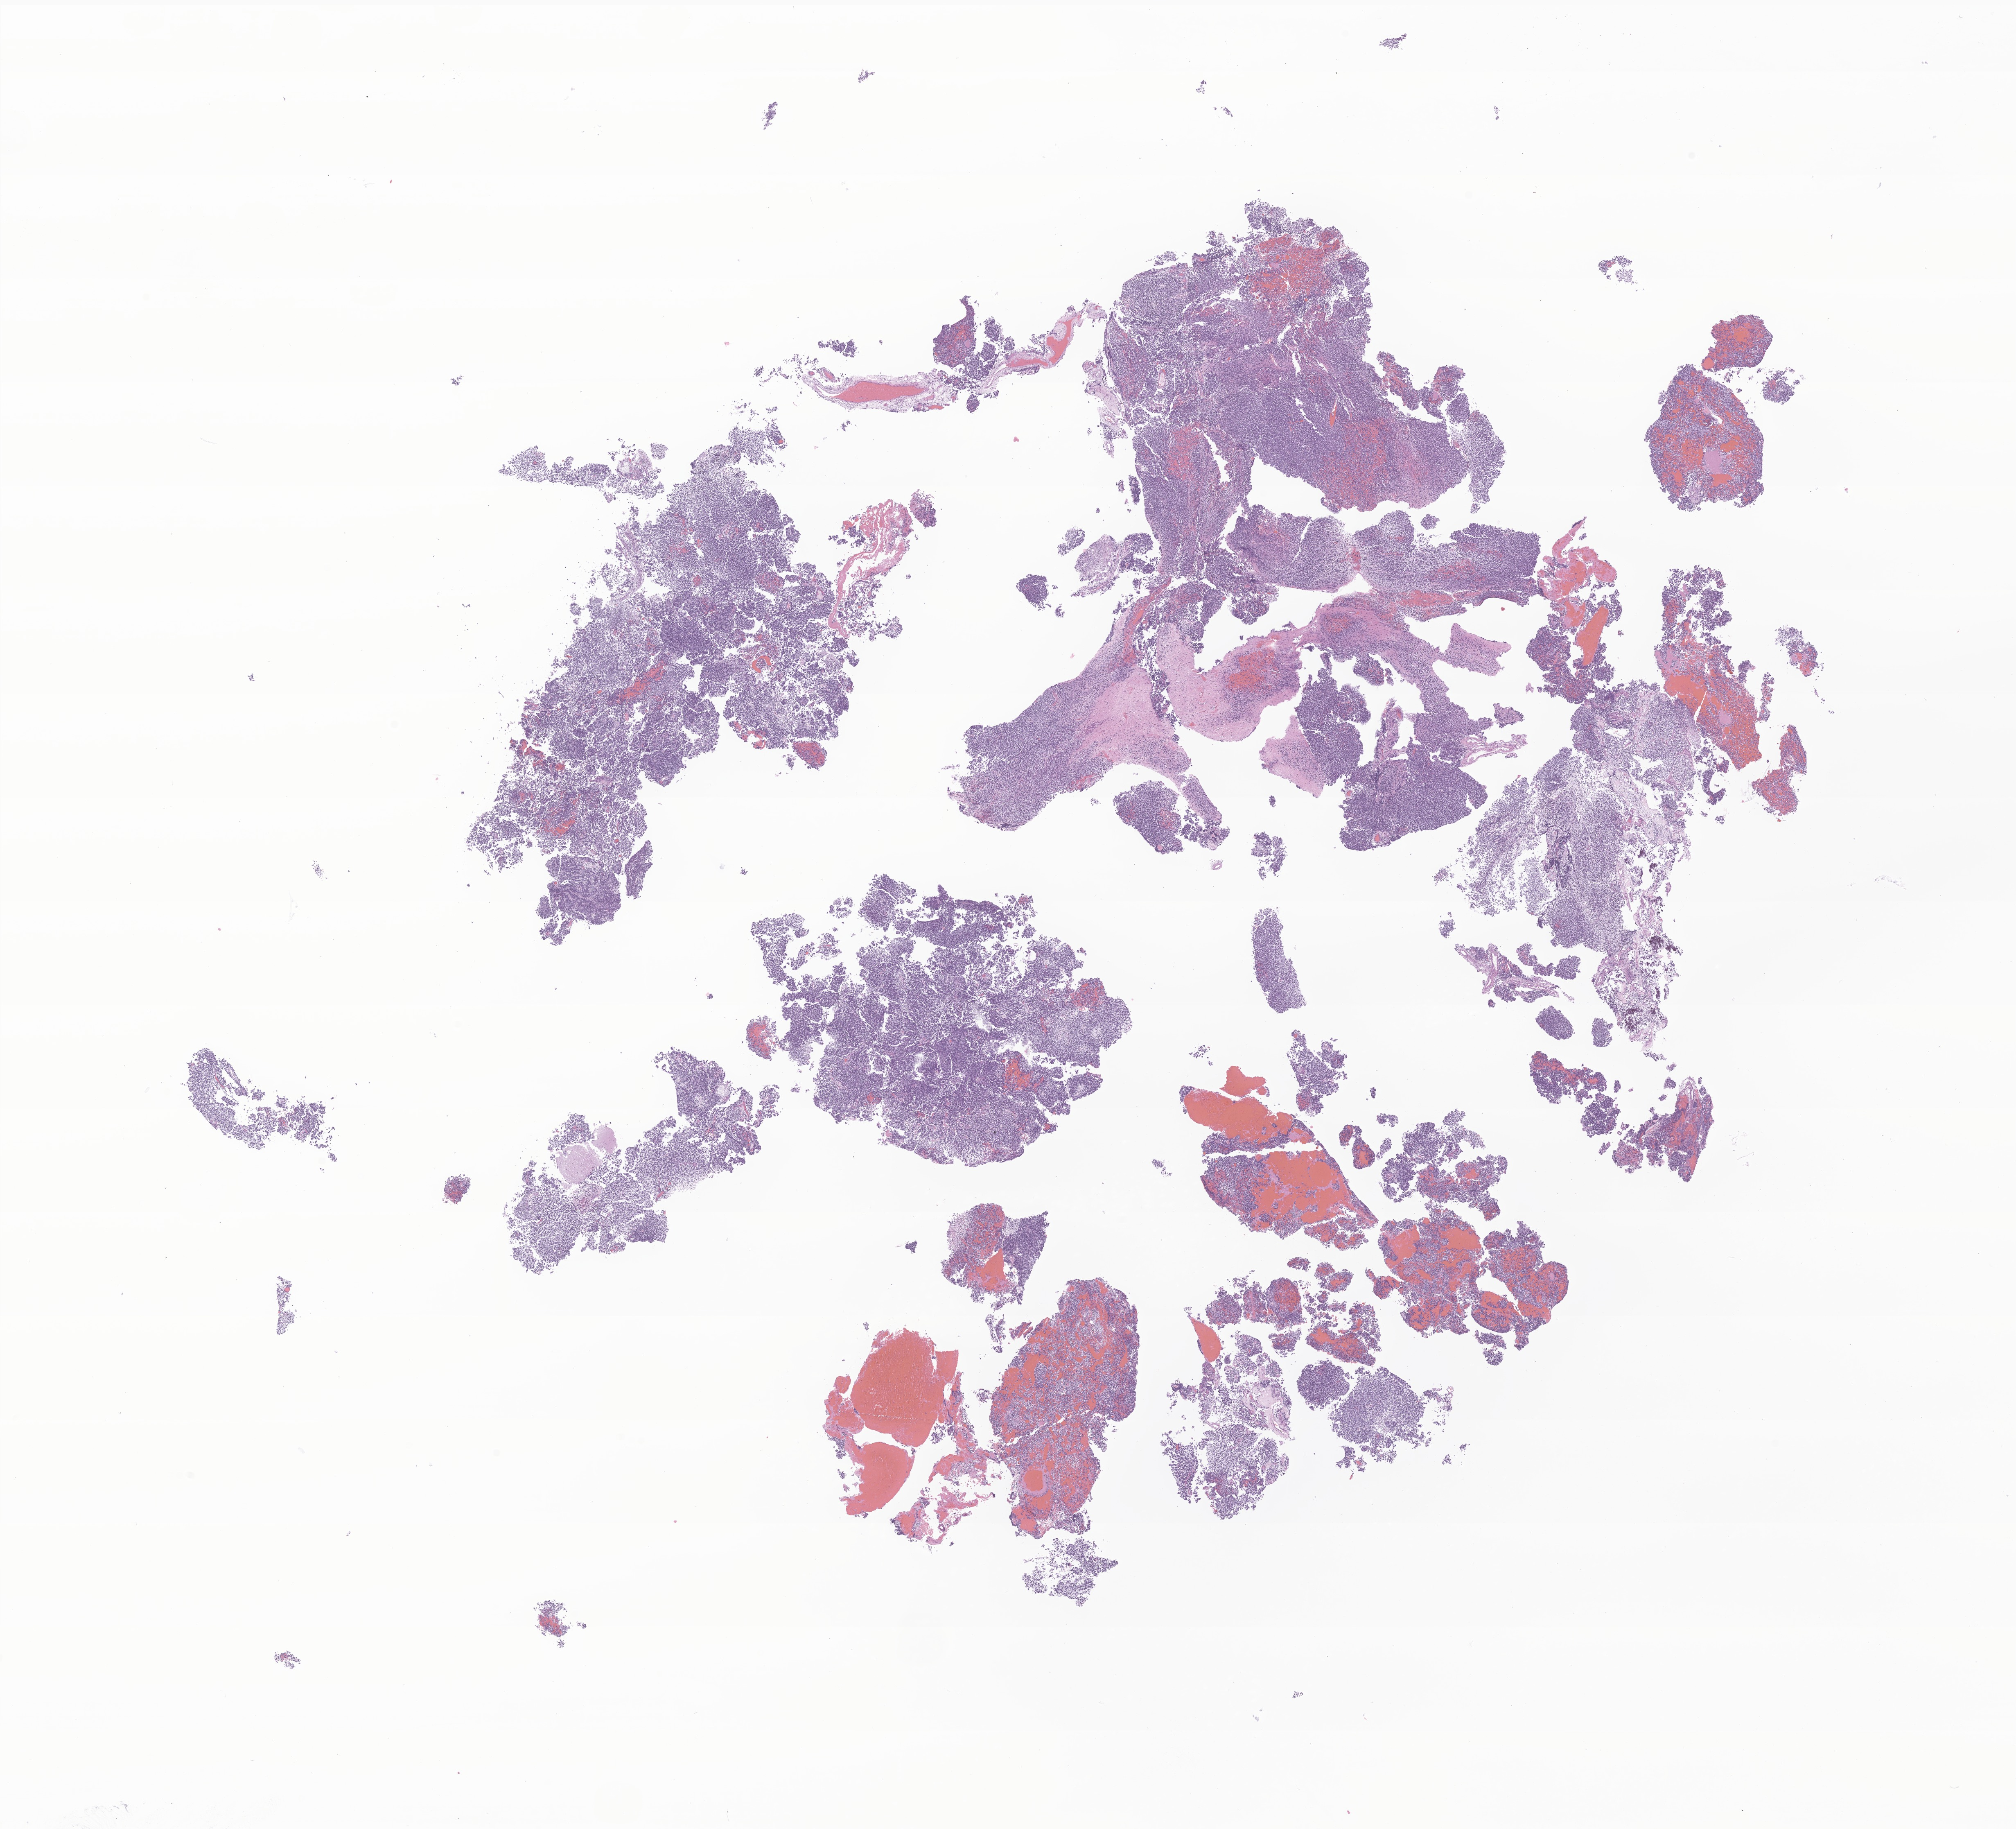
Digitized hematoxylin and eosin (H&E)-stained section of tumor tissue from the brain — low-resolution overview of the scanned area, about 20.8 x 18.8 mm, formalin-fixed paraffin-embedded section. Patient female; age 153 months (12 years 9 months).
- diagnosis (ICD-O-3 morphology term): Medulloblastoma, NOS